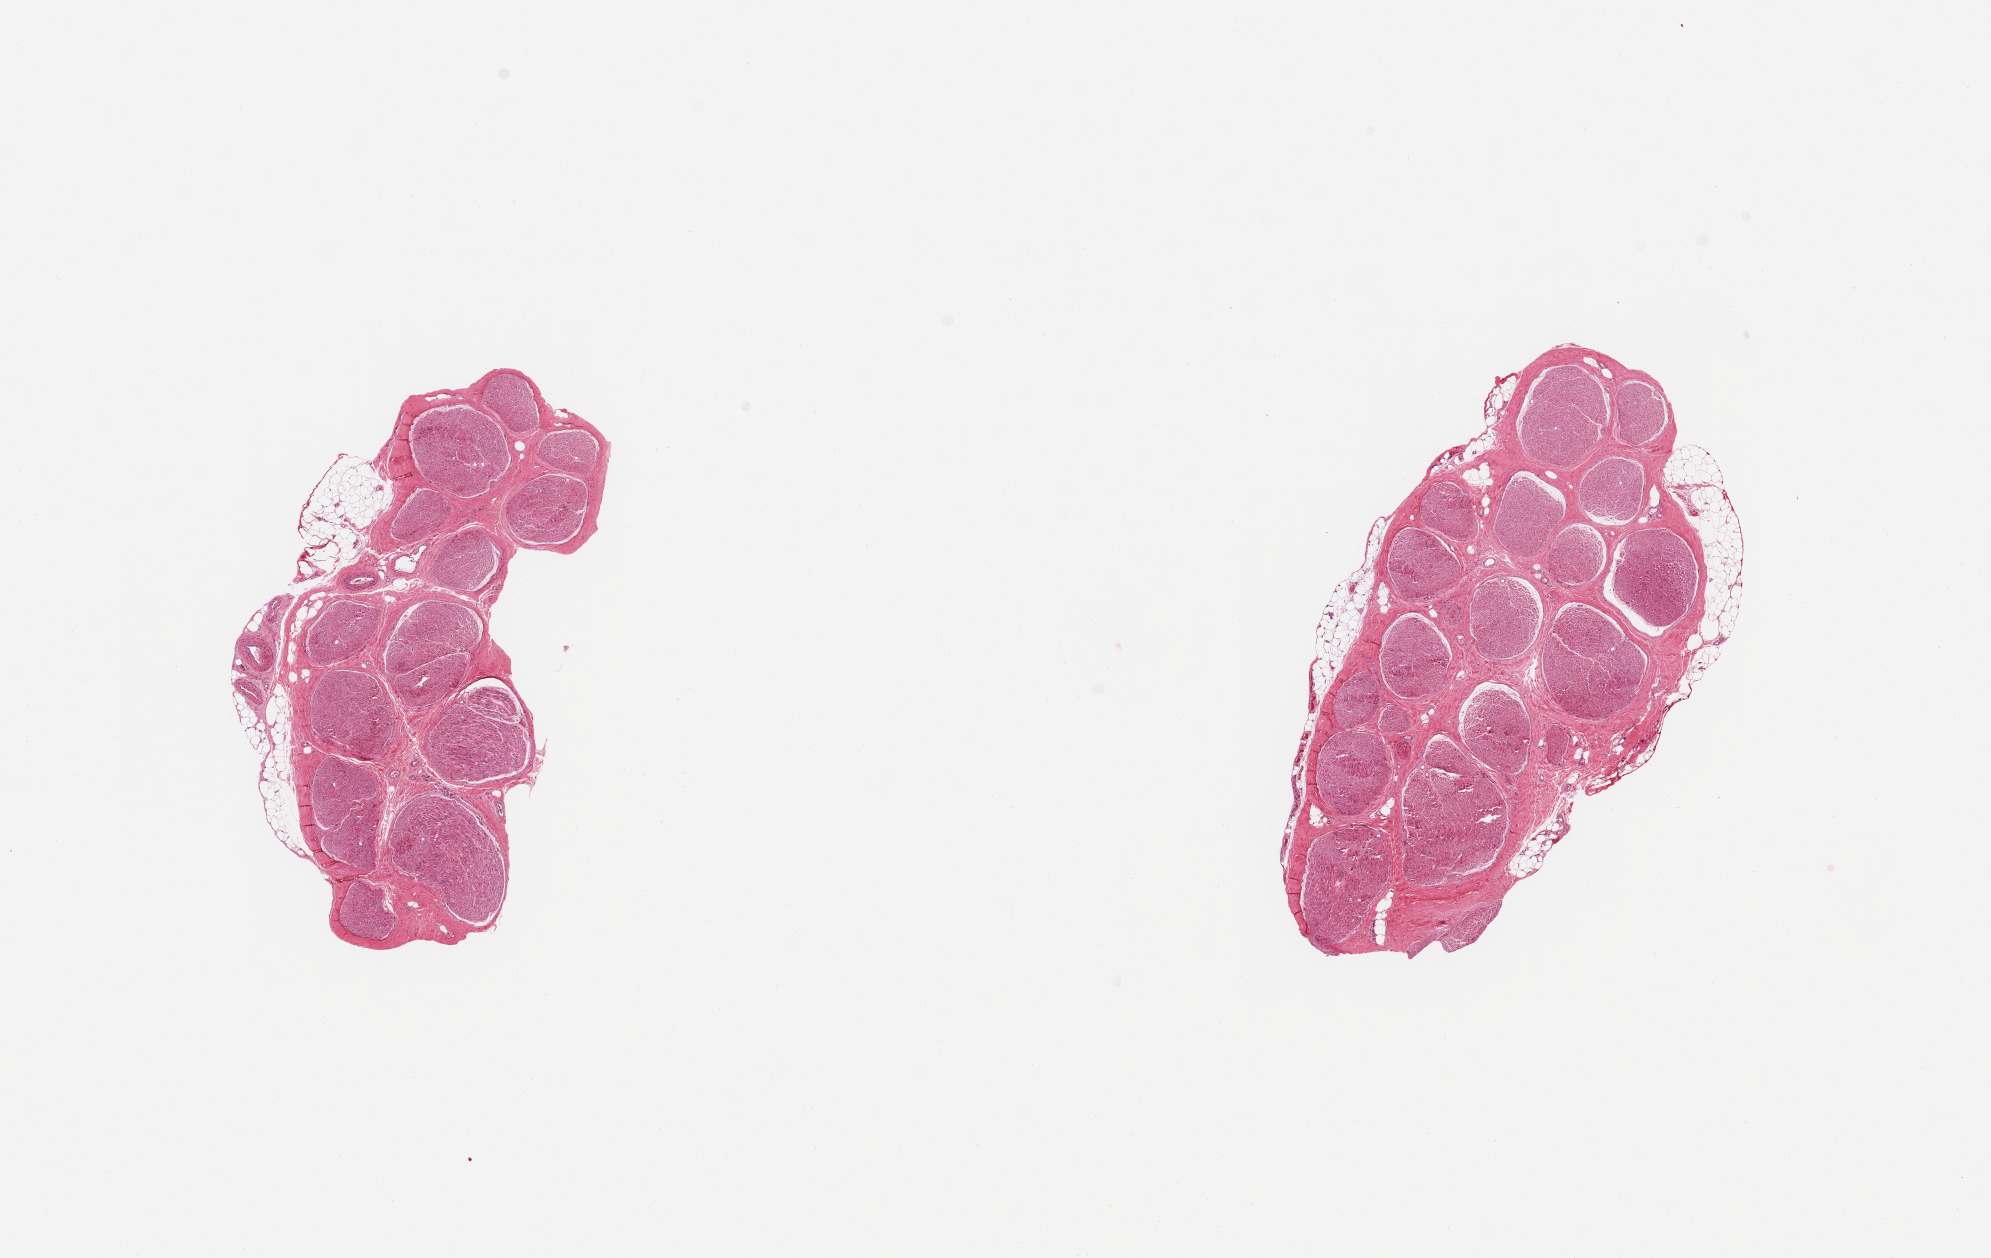
Digitized haematoxylin and eosin-stained section, shown as a low-resolution overview of the whole scanned area (about 15.8 x 10.0 mm, slide scanned at 20x), PAXgene-fixed, paraffin-embedded tissue, target tissue: tibial nerve, donor tissue sample. Donor sex: male.
• review note (as recorded): 2 pieces; up to ~0.4 mm attached fat